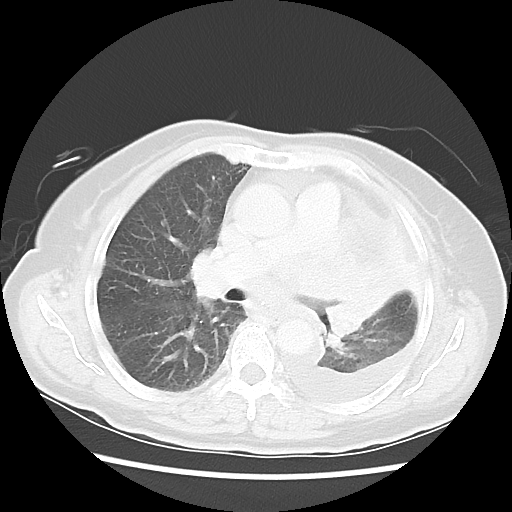
Chest CT, one axial slice. Position 32 of 52 along the scan axis. Reconstruction kernel LUNG. Lung window (W 1500 / L -600 HU). 5 mm slice thickness. 512 × 512 image matrix, field of view 336 × 336 mm. Patient: female, 72 years. Case-level facts recorded for this patient, not image findings: clinical TNM (as recorded): T4 N3 M1b; histopathological grade: G3.
Structures marked on this image (rectangle marked by the reading radiologist):
- lung tumour (recorded histology: large cell carcinoma): bounding box <306,248,407,348> (left, top, right, bottom; pixels)